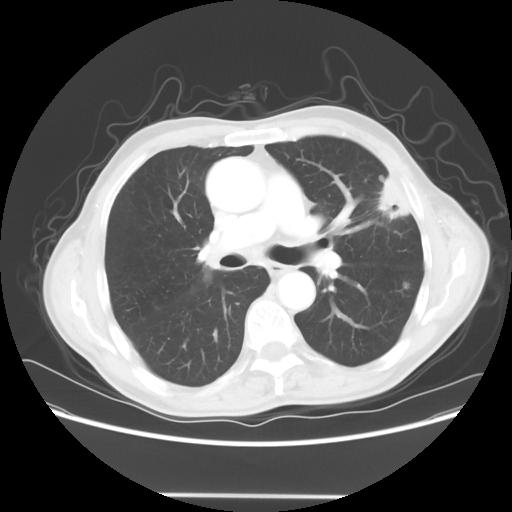
Chest CT, one axial slice. Slice 37 of 64 in the series (ordered by position). Lung window (W 1500 / L -600 HU). 5 mm slice thickness. 512 × 512 image matrix, field of view 392 × 392 mm. Male patient, age 71 years. Case-level facts recorded for this patient, not image findings: clinical TNM (as recorded): T1c N0 M0.
Structures marked on this image (rectangle marked by the reading radiologist):
- lung tumour (recorded histology: adenocarcinoma): bounding box [x1, y1, x2, y2] px = [369, 158, 423, 229]